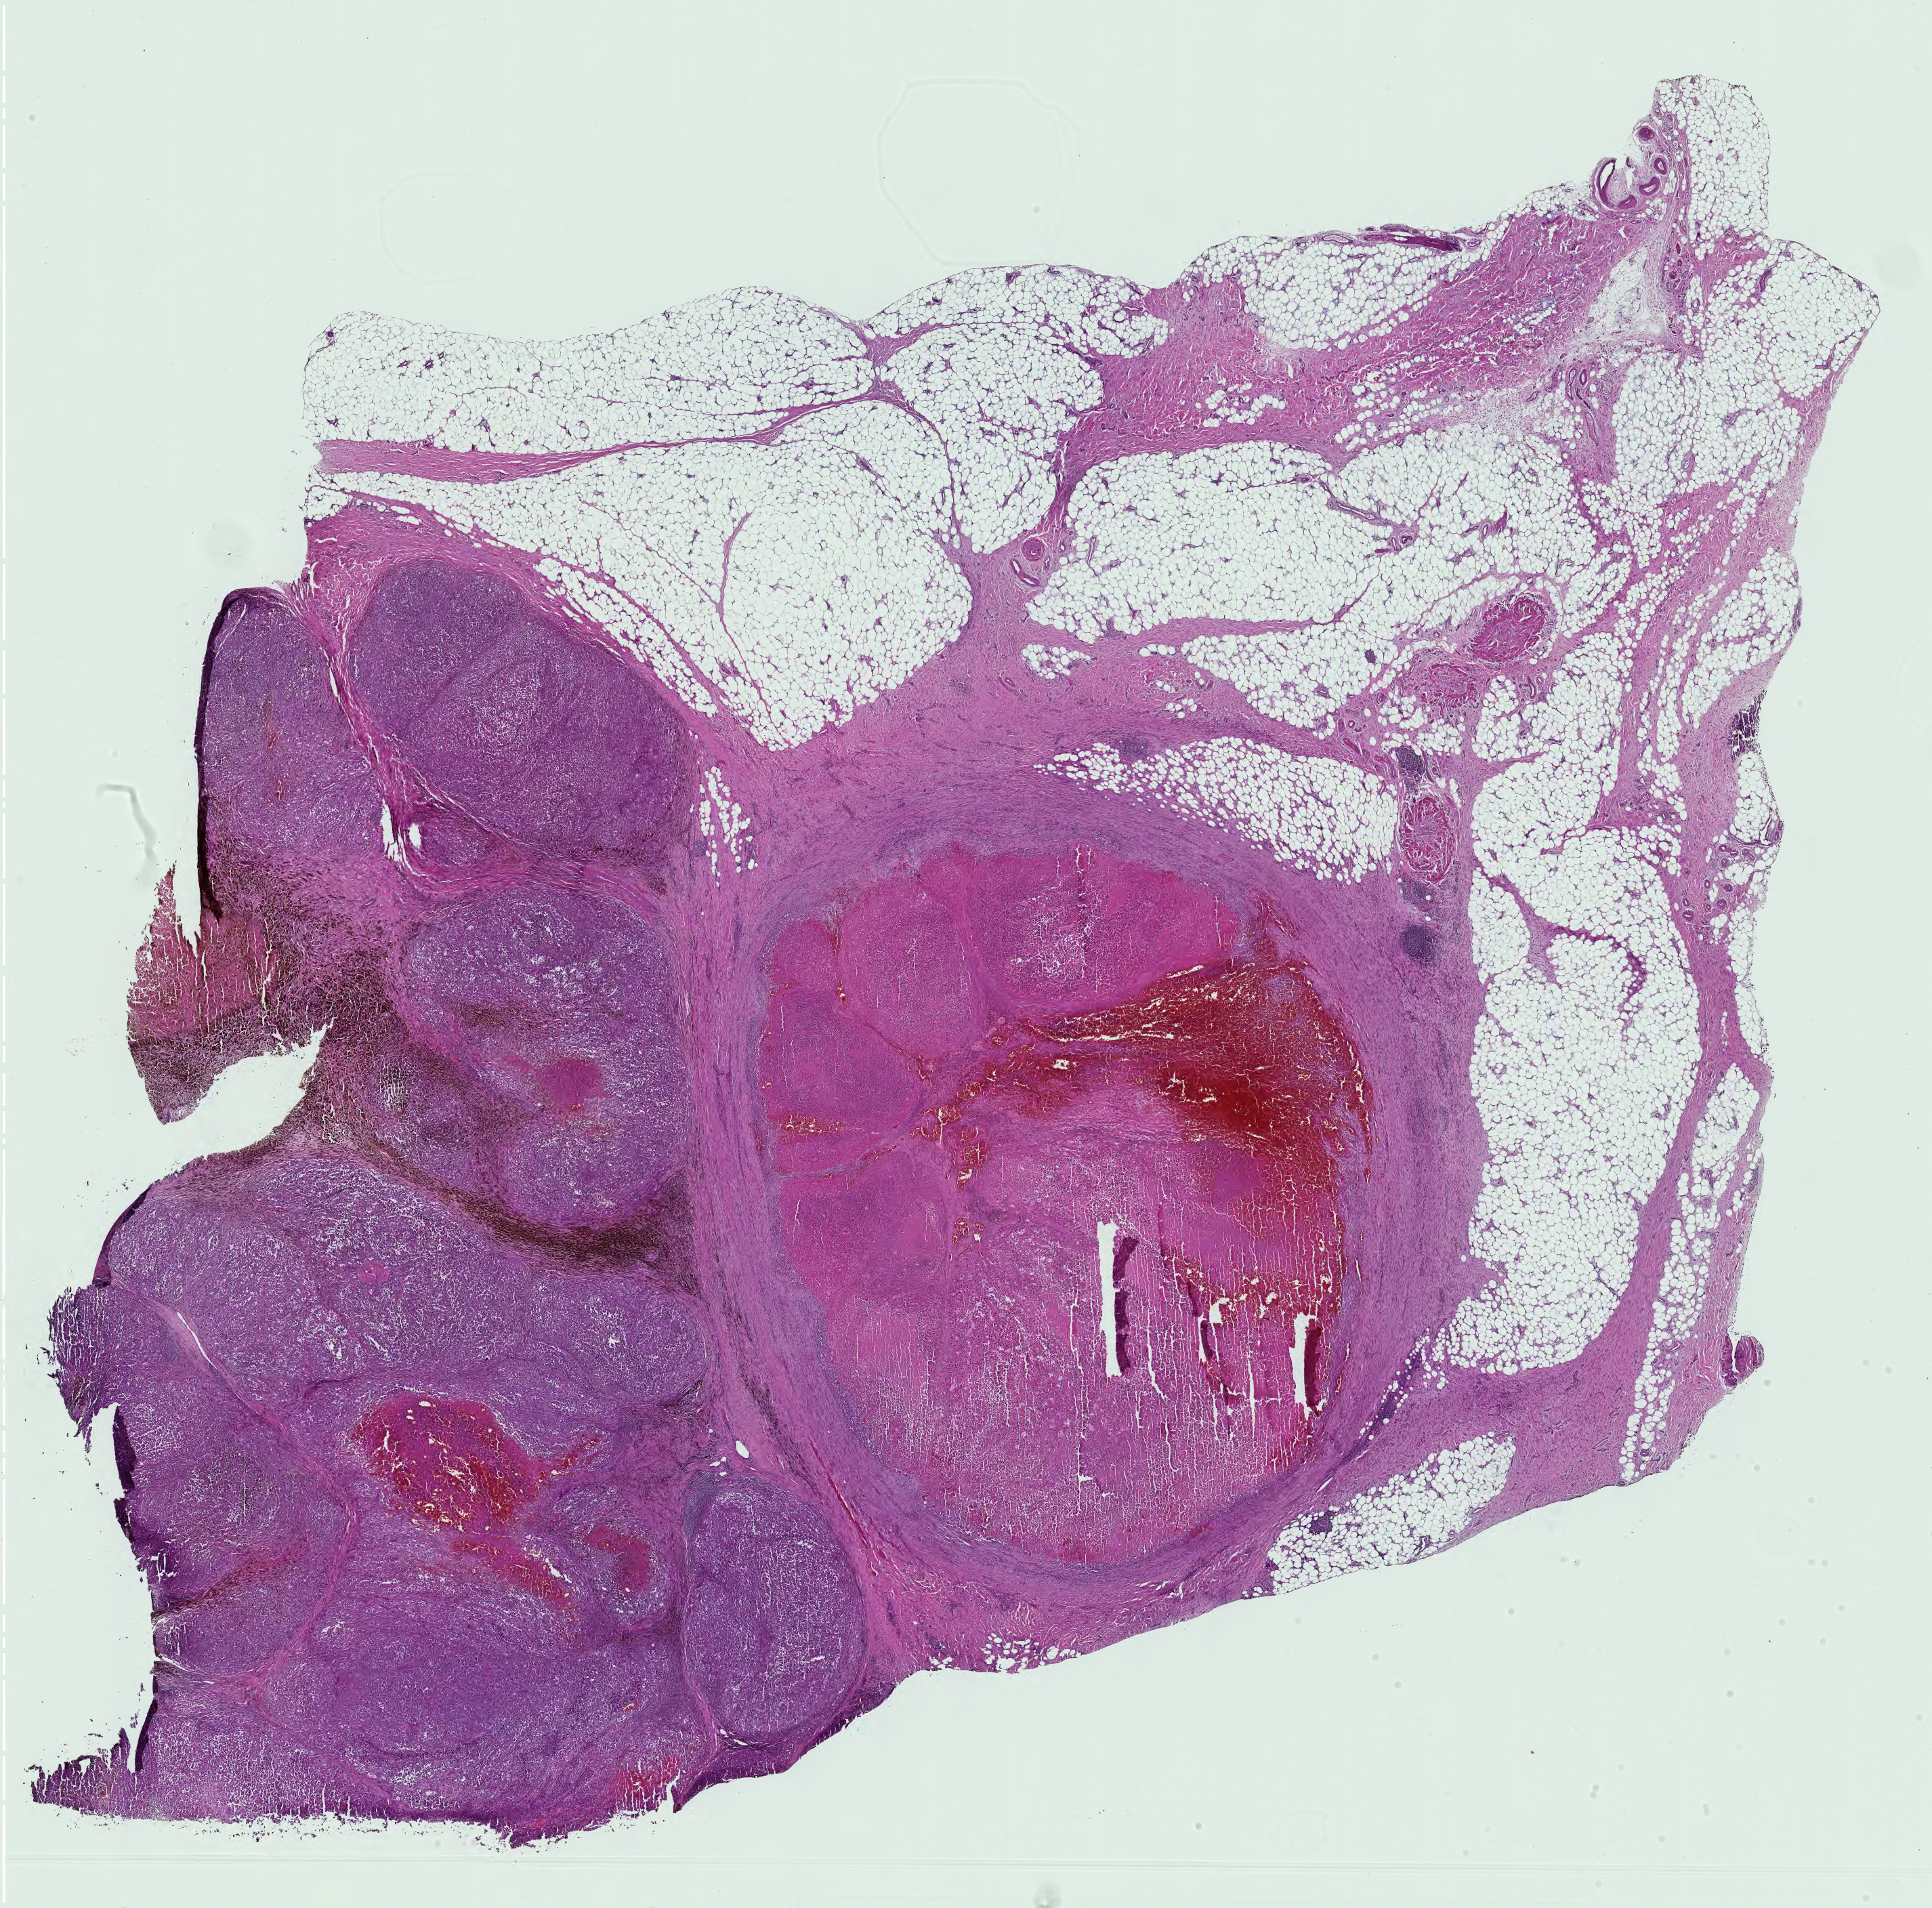
Digitized H&E-stained tissue section (whole slide) — low-resolution overview of the scanned area, about 20.7 x 20.4 mm (acquisition: 40x scan). FFPE section. Sample: primary tumour, skin. Patient: male, age at initial diagnosis 49 years.
- pathologic diagnosis: Malignant melanoma, NOS